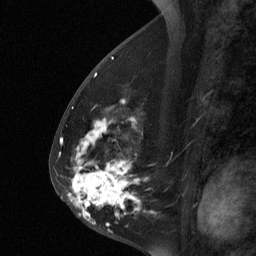
Breast MRI (dynamic contrast-enhanced), one sagittal slice; position 30 of 64 along the scan axis; dynamic contrast-enhanced study with each time point stored as its own series, time point 2 of 3 at this slice position (early post-contrast, ordered by acquisition time); 1.5 T; TE 4.8 ms, TR 27 ms; 256 × 256 image matrix, field of view 180 × 180 mm. Female patient, age 56 years. From the clinical record (not read from this slice): setting: breast cancer imaged before/during neoadjuvant chemotherapy; receptor status: HER2-positive.
Structures marked on this image (semi-automatically segmented with operator editing):
- analysis volume of interest (the breast-tissue region the enhancement analysis was run in; not a lesion): bounding box [x1, y1, x2, y2] px = [59, 104, 155, 229]
- tumour enhancement mask (voxels above the 90 % enhancement threshold inside the analysis volume of interest): [68, 146, 134, 224]